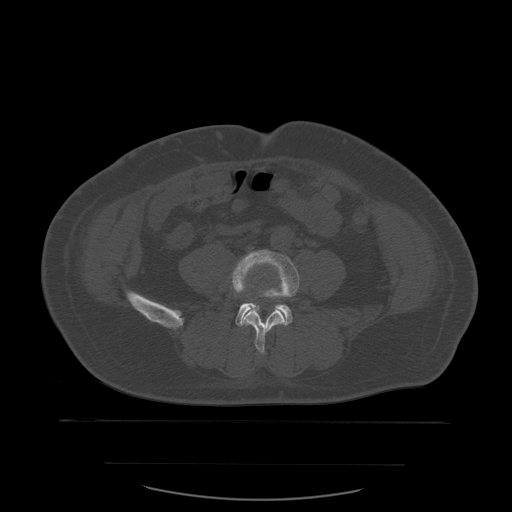
CT including the spine, one axial slice. Slice 154 of 590 in the series (ordered by position). Bone window (W 1800 / L 400 HU). 512 × 512 image matrix, field of view 479 × 479 mm. Patient age 71 years. Case-level facts recorded for this patient, not image findings: primary cancer: lung; vertebrae with lytic lesions (as recorded): T1, T2, L5, S1.
Structures marked on this image (semi-automatic segmentation, software-assisted and operator-edited):
- L4 vertebra: bounding box [x1, y1, x2, y2] px = [232, 250, 299, 354]
- L5 vertebra: [235, 297, 293, 327]